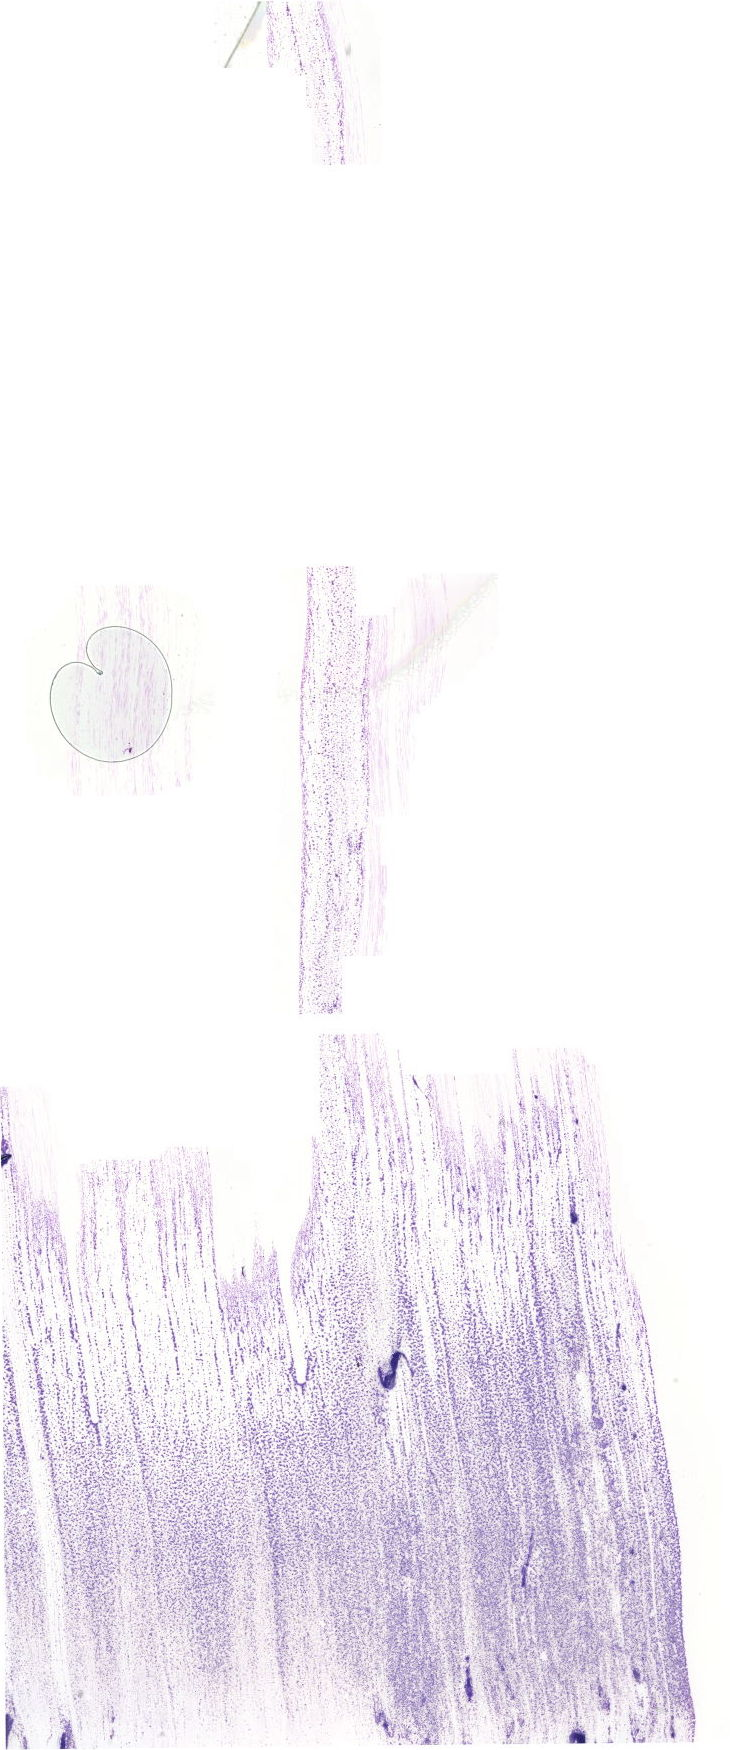
Whole-slide image of a May-Grünwald–Giemsa-stained bone marrow aspirate smear — low-resolution overview of the scanned area, about 20.7 x 49.6 mm. Patient sex: male.
- diagnosis: Chronic Phase Chronic Myeloid Leukemia, BCR-ABL1 Positive